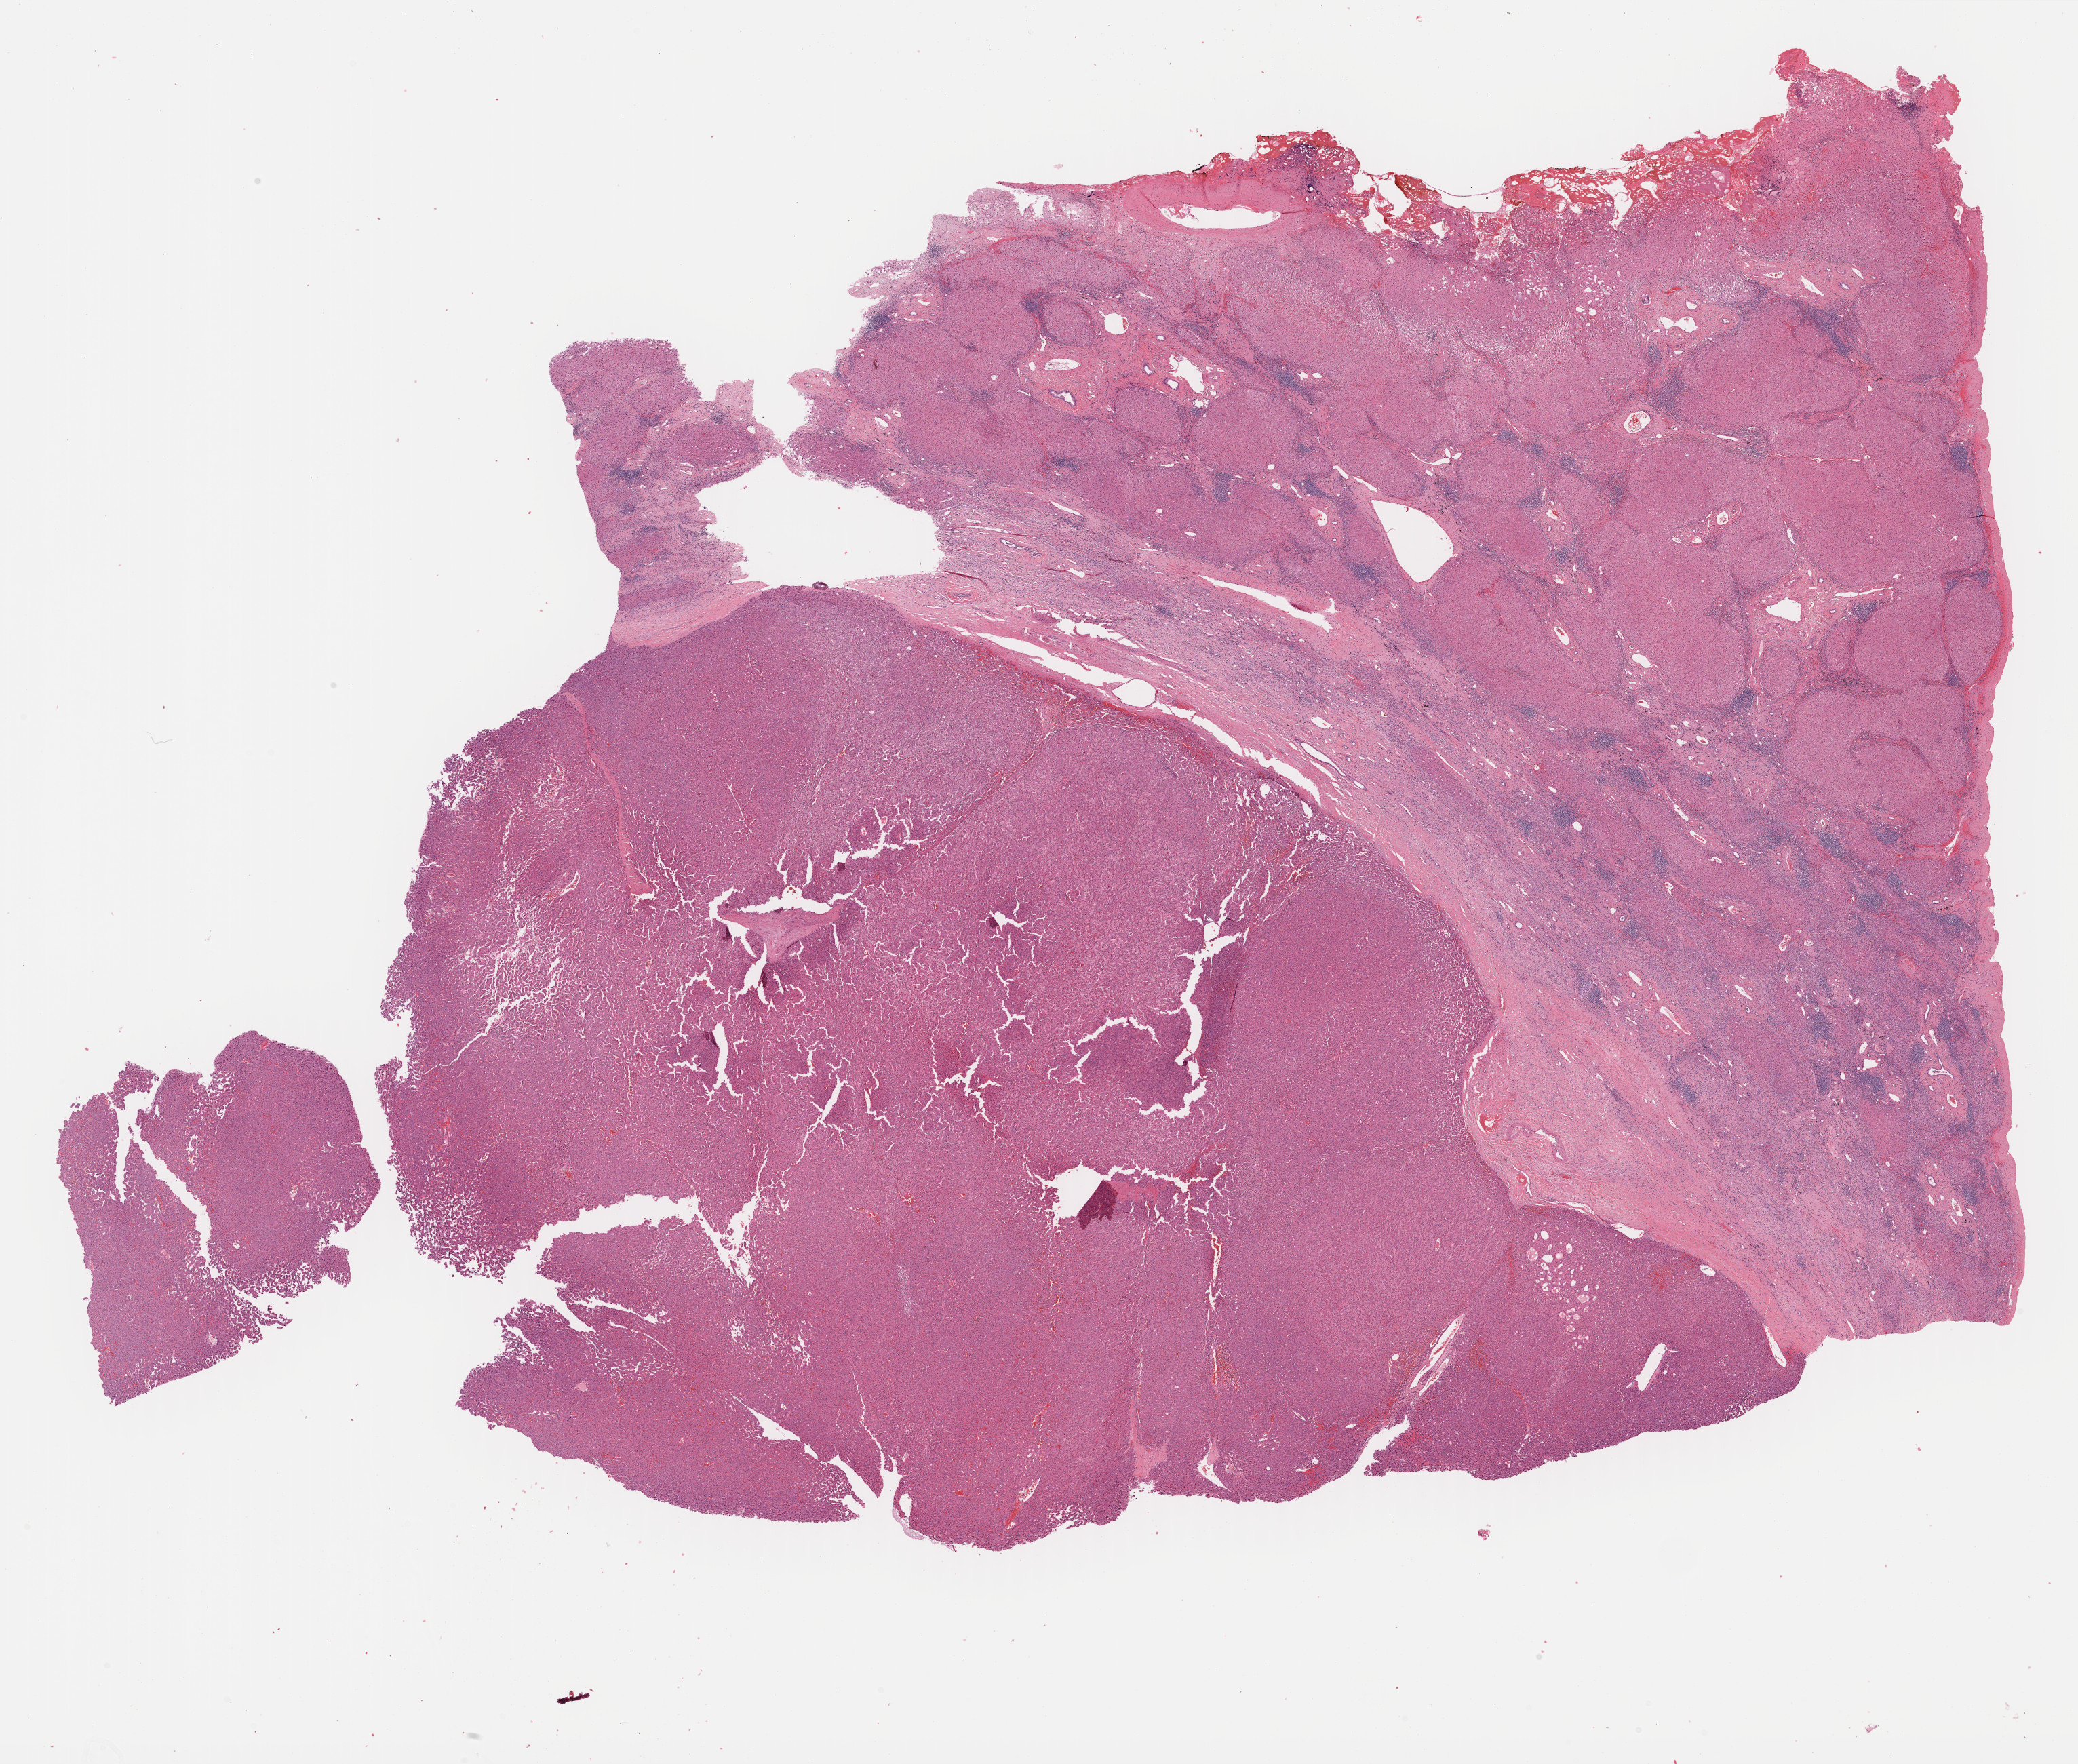
Digitized H&E-stained tissue section (whole slide), low-resolution overview of the scanned area, about 24.8 x 21.1 mm; FFPE section; primary tumour sample from the liver. Patient: male, age at initial diagnosis 72 years. Histologic grade: G2 (moderately differentiated).
AJCC pathologic stage: I (7th edition). Histologic diagnosis: Hepatocellular carcinoma, NOS.